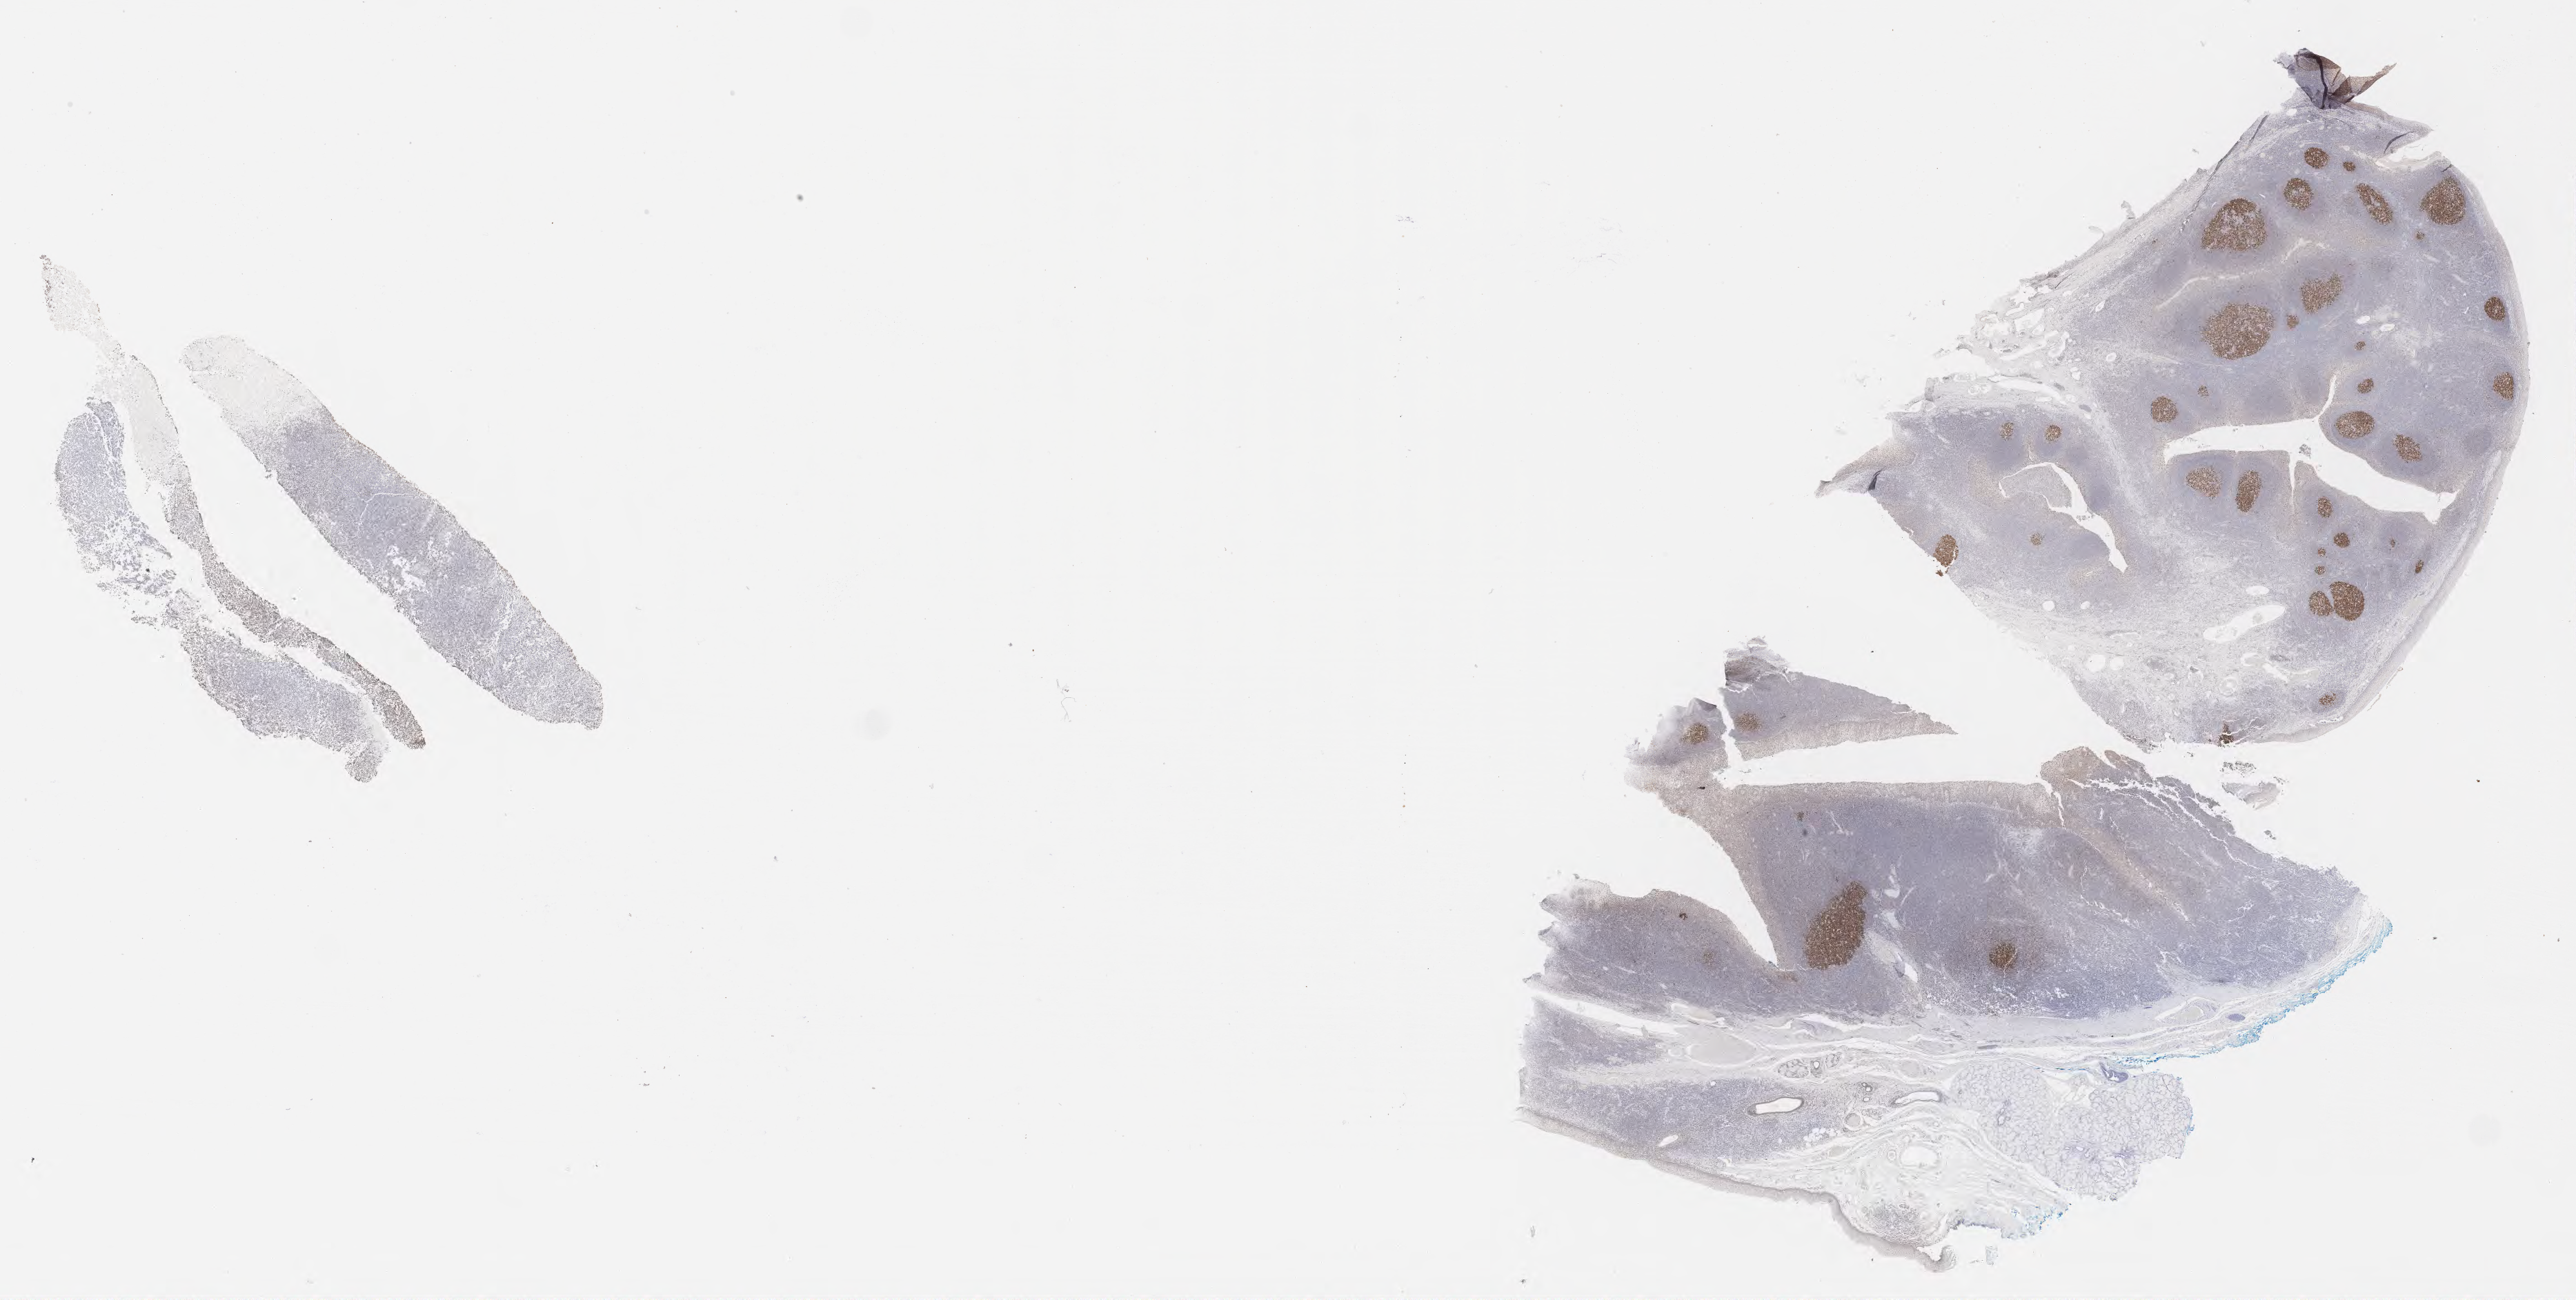
Whole-slide image, immunohistochemical stain for BCL6 — whole scanned area (about 30.2 x 15.2 mm) shown as a low-resolution overview, tumor tissue. Patient: female, aged 18.
Histologic diagnosis: Burkitt lymphoma, NOS.